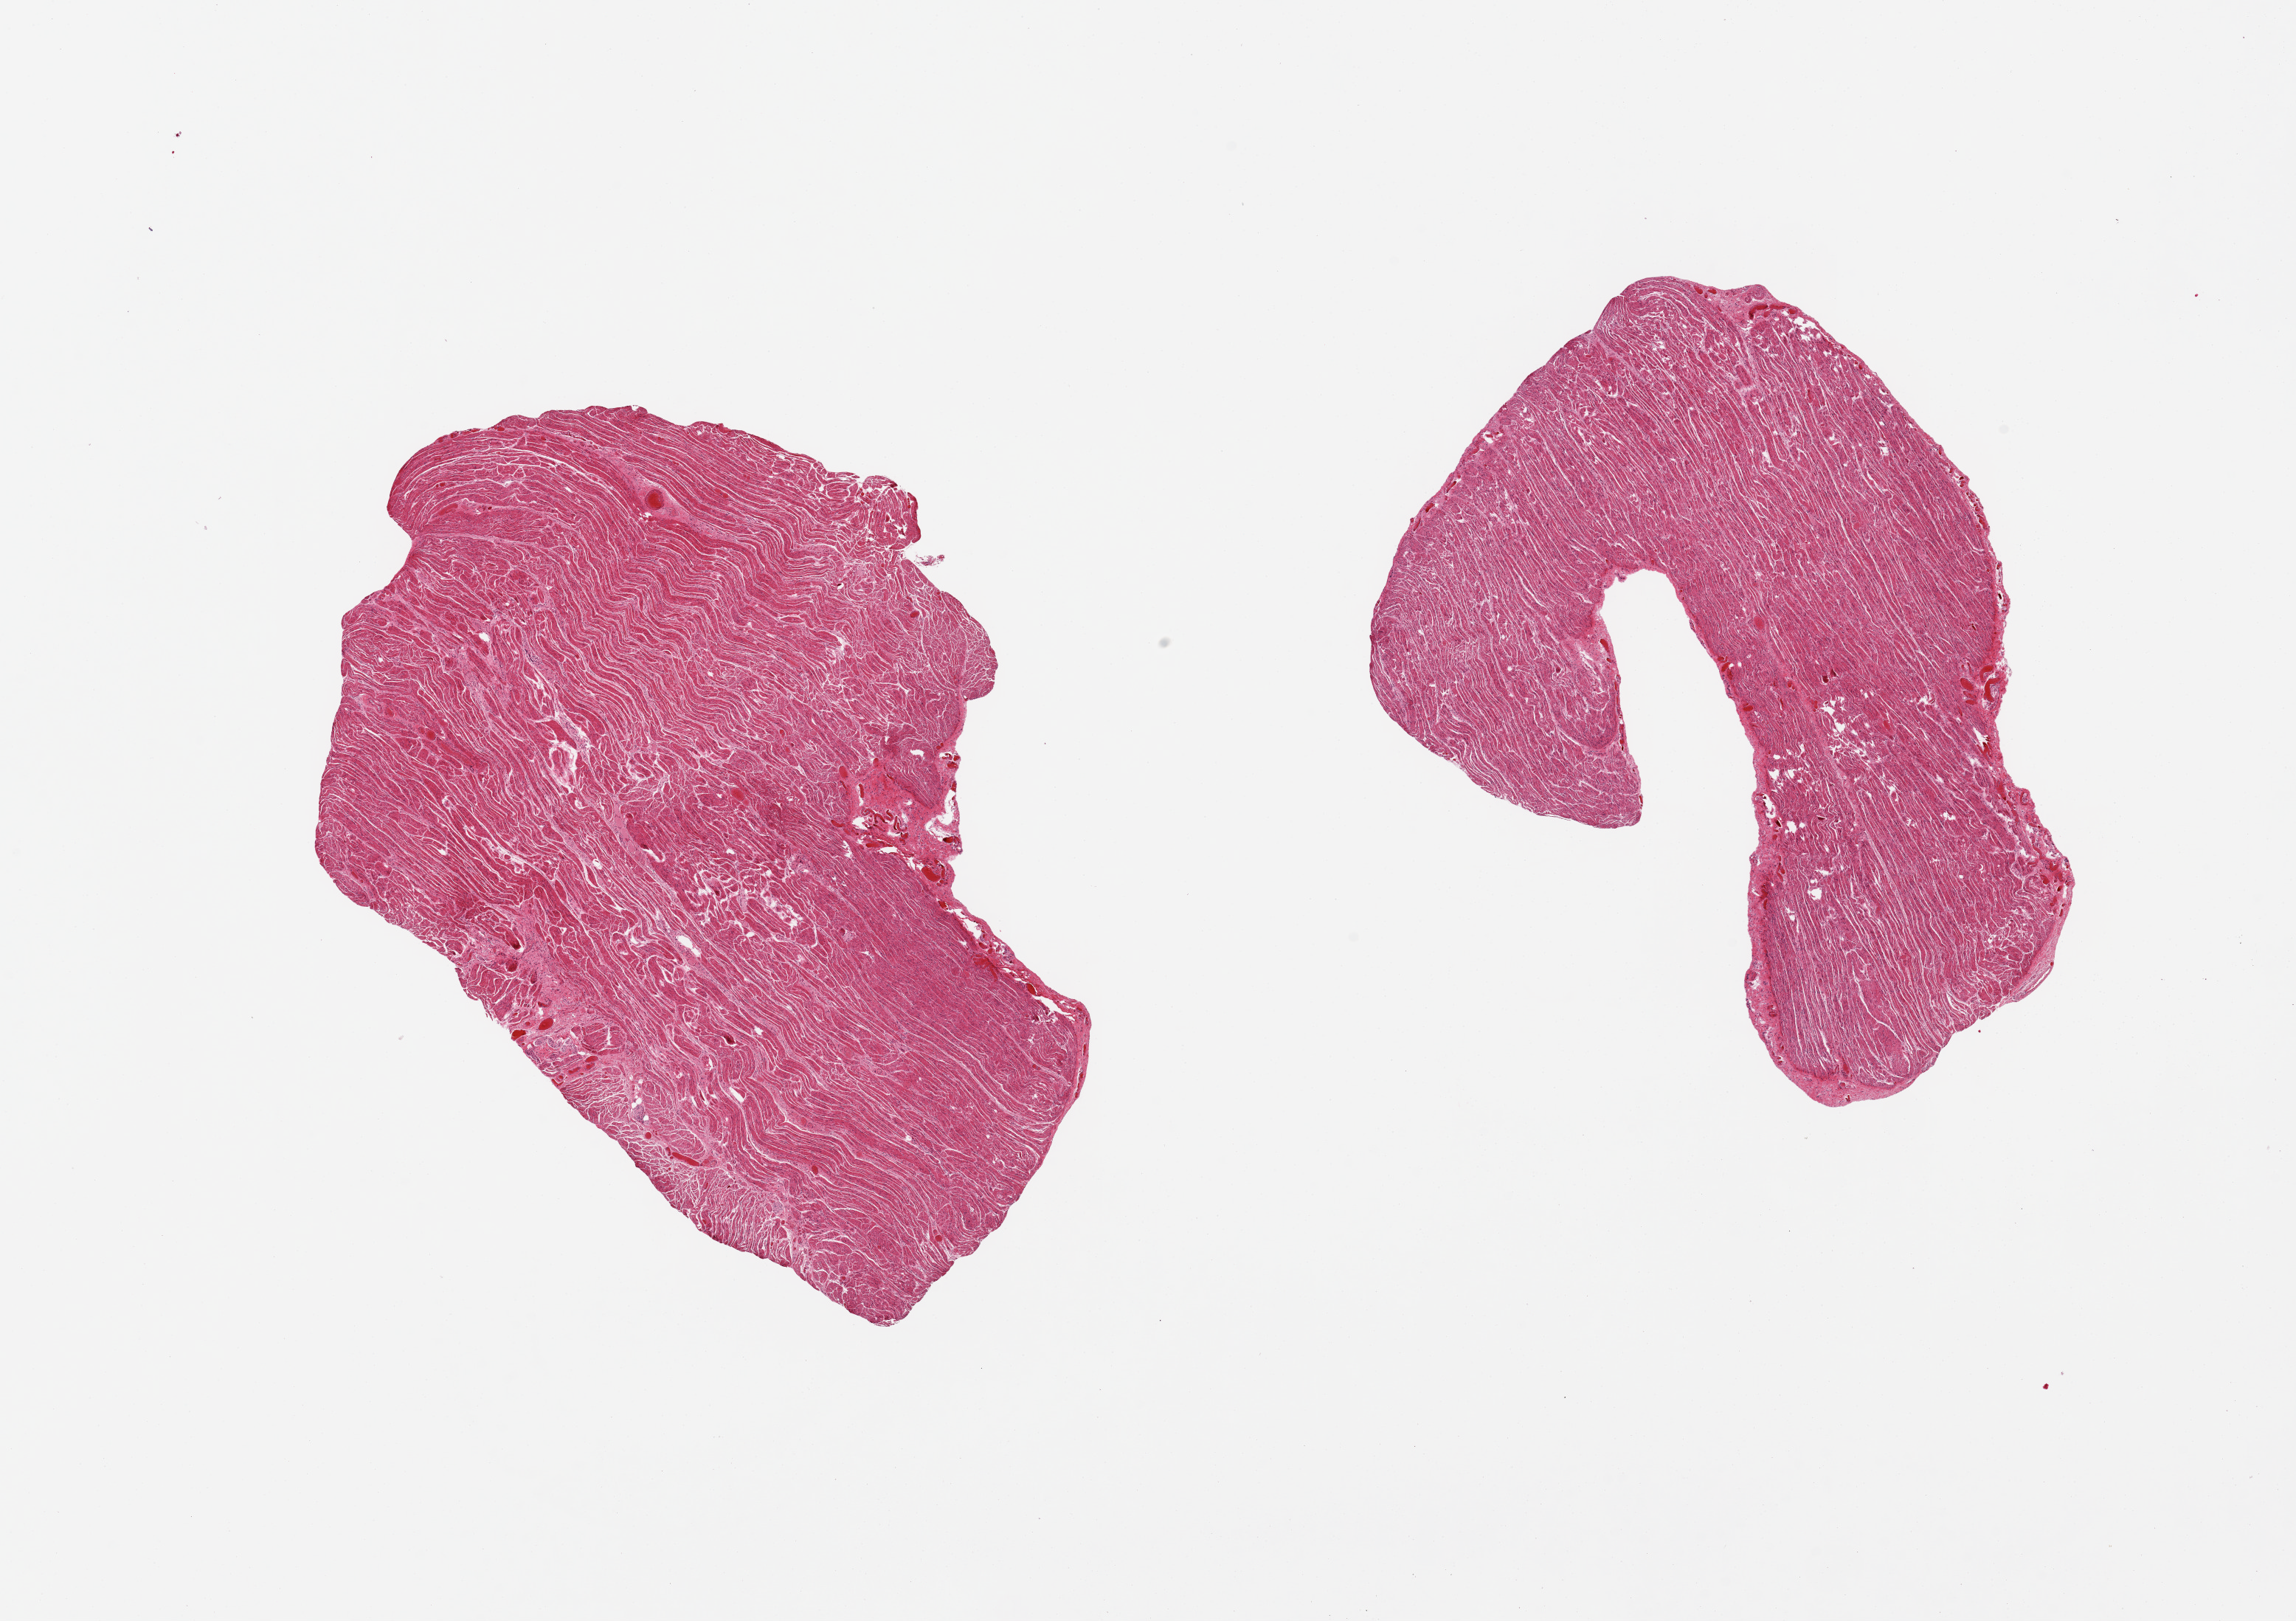
Whole-slide image, H&E stain, shown as a low-resolution overview of the whole scanned area (about 24.6 x 17.4 mm), PAXgene-fixed paraffin-embedded (PFPE) section, section of gastroesophageal junction (target tissue), tissue donor sample. Donor sex: female.
• reviewer comment on this tissue sample: 2 pieces, all muscularis